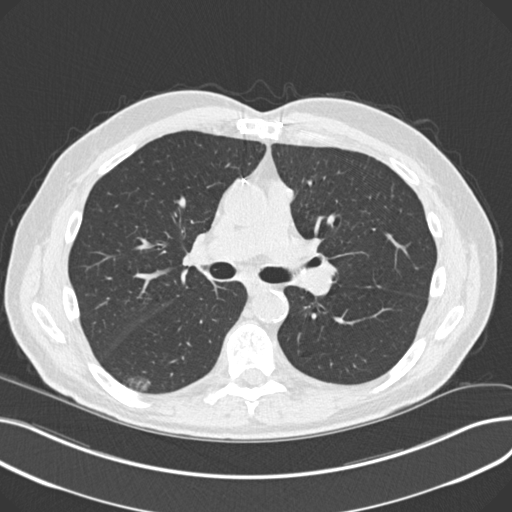
Chest CT (low-dose screening protocol), one axial image; third screening round (two years after baseline); lung window (W 1500 / L -600 HU); 2 mm slice thickness; slice 102 of 230 in the series; 512 × 512 image matrix. Male participant, aged 68 years at enrolment. Current smoker at enrolment.
Expert reader's lesion annotation, bounding box <121,367,165,398> (left, top, right, bottom; pixels). The screening reader recorded 5 non-calcified nodules or masses ≥4 mm on this exam (right upper lobe, left upper lobe, right upper lobe, right lower lobe, right upper lobe); which of them this box marks is not recorded. Participant outcome: lung cancer diagnosed 247 days after this screen — non-small cell carcinoma, right lower lobe, poorly differentiated (G3), stage IA (AJCC 6th edition), 23 mm at pathology.